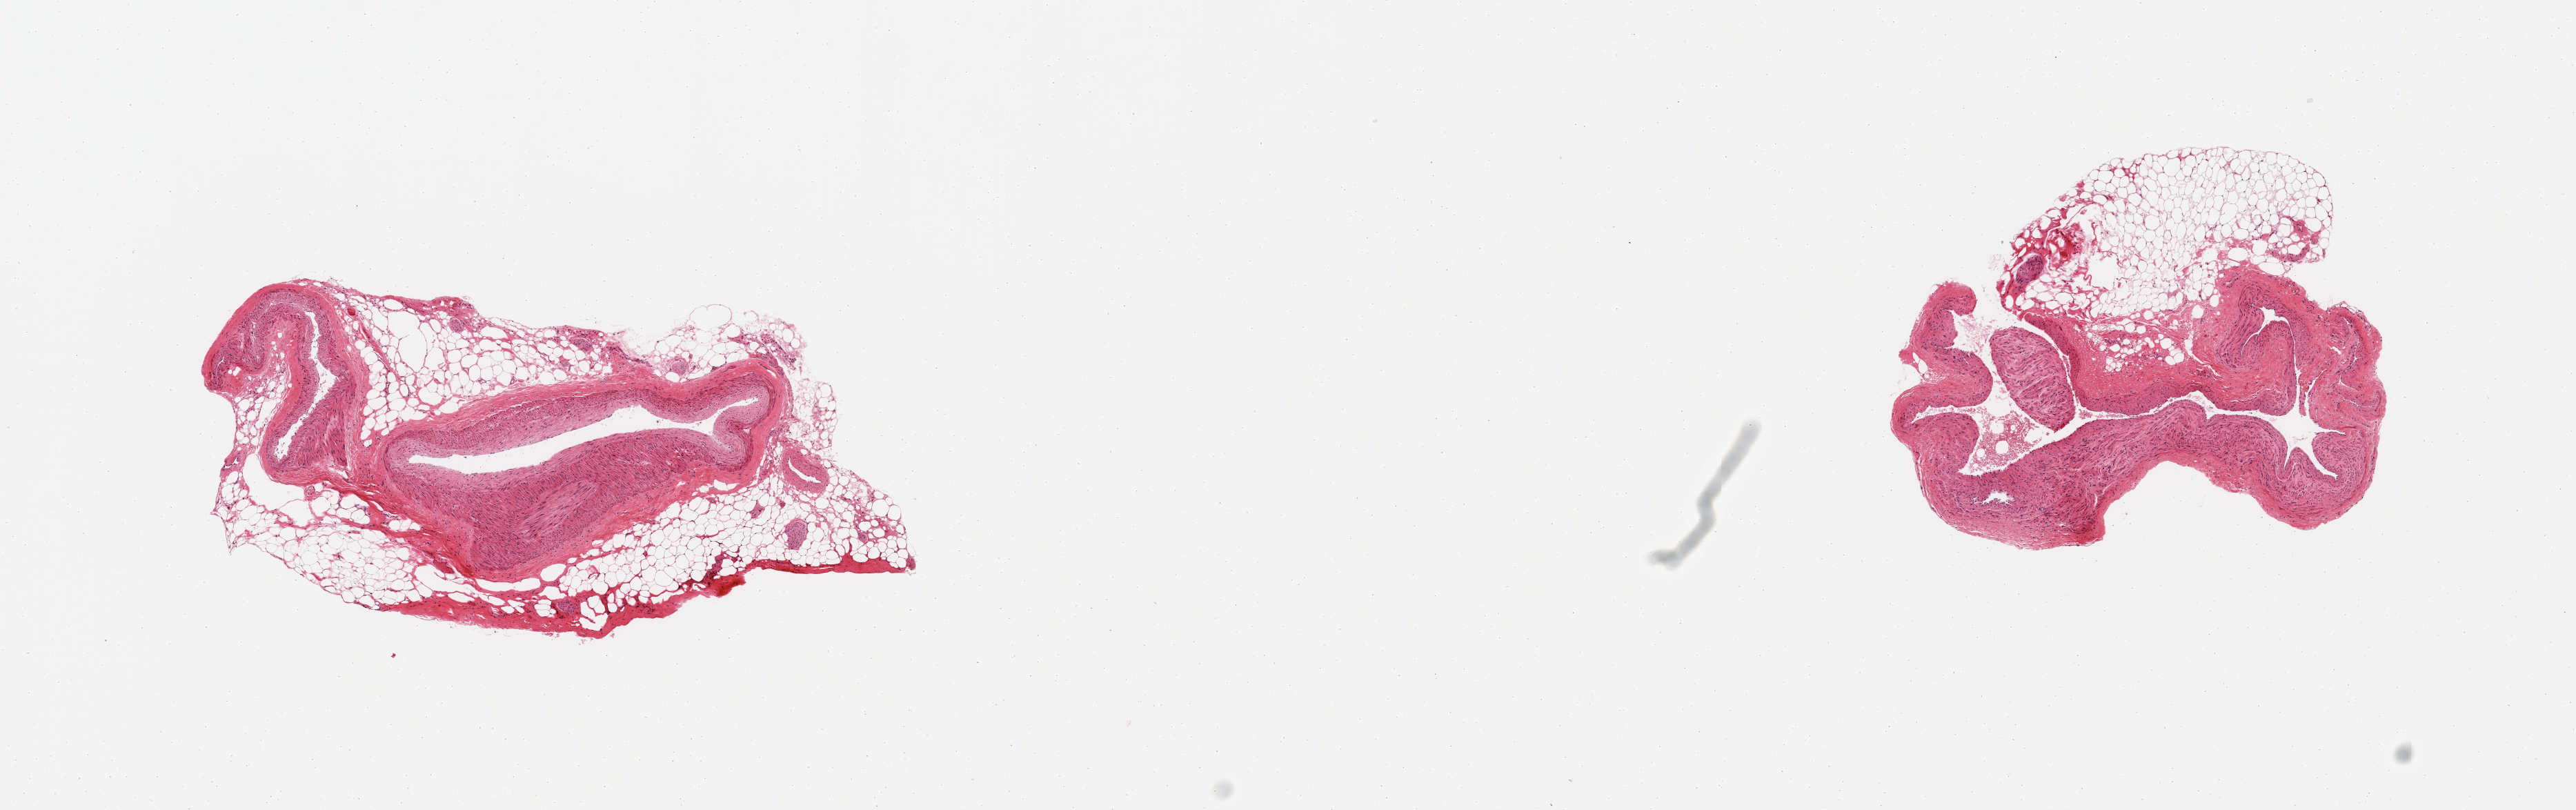
Whole-slide image, haematoxylin and eosin stain — low-resolution overview of the scanned area, about 14.8 x 4.6 mm, PAXgene-fixed paraffin-embedded (PFPE) section, sampled site (target tissue): coronary artery, tissue donor sample. Donor sex: female.
Reviewer comment on this tissue sample: 2 pieces, no atherosis; adherent fat up to ~1mm.